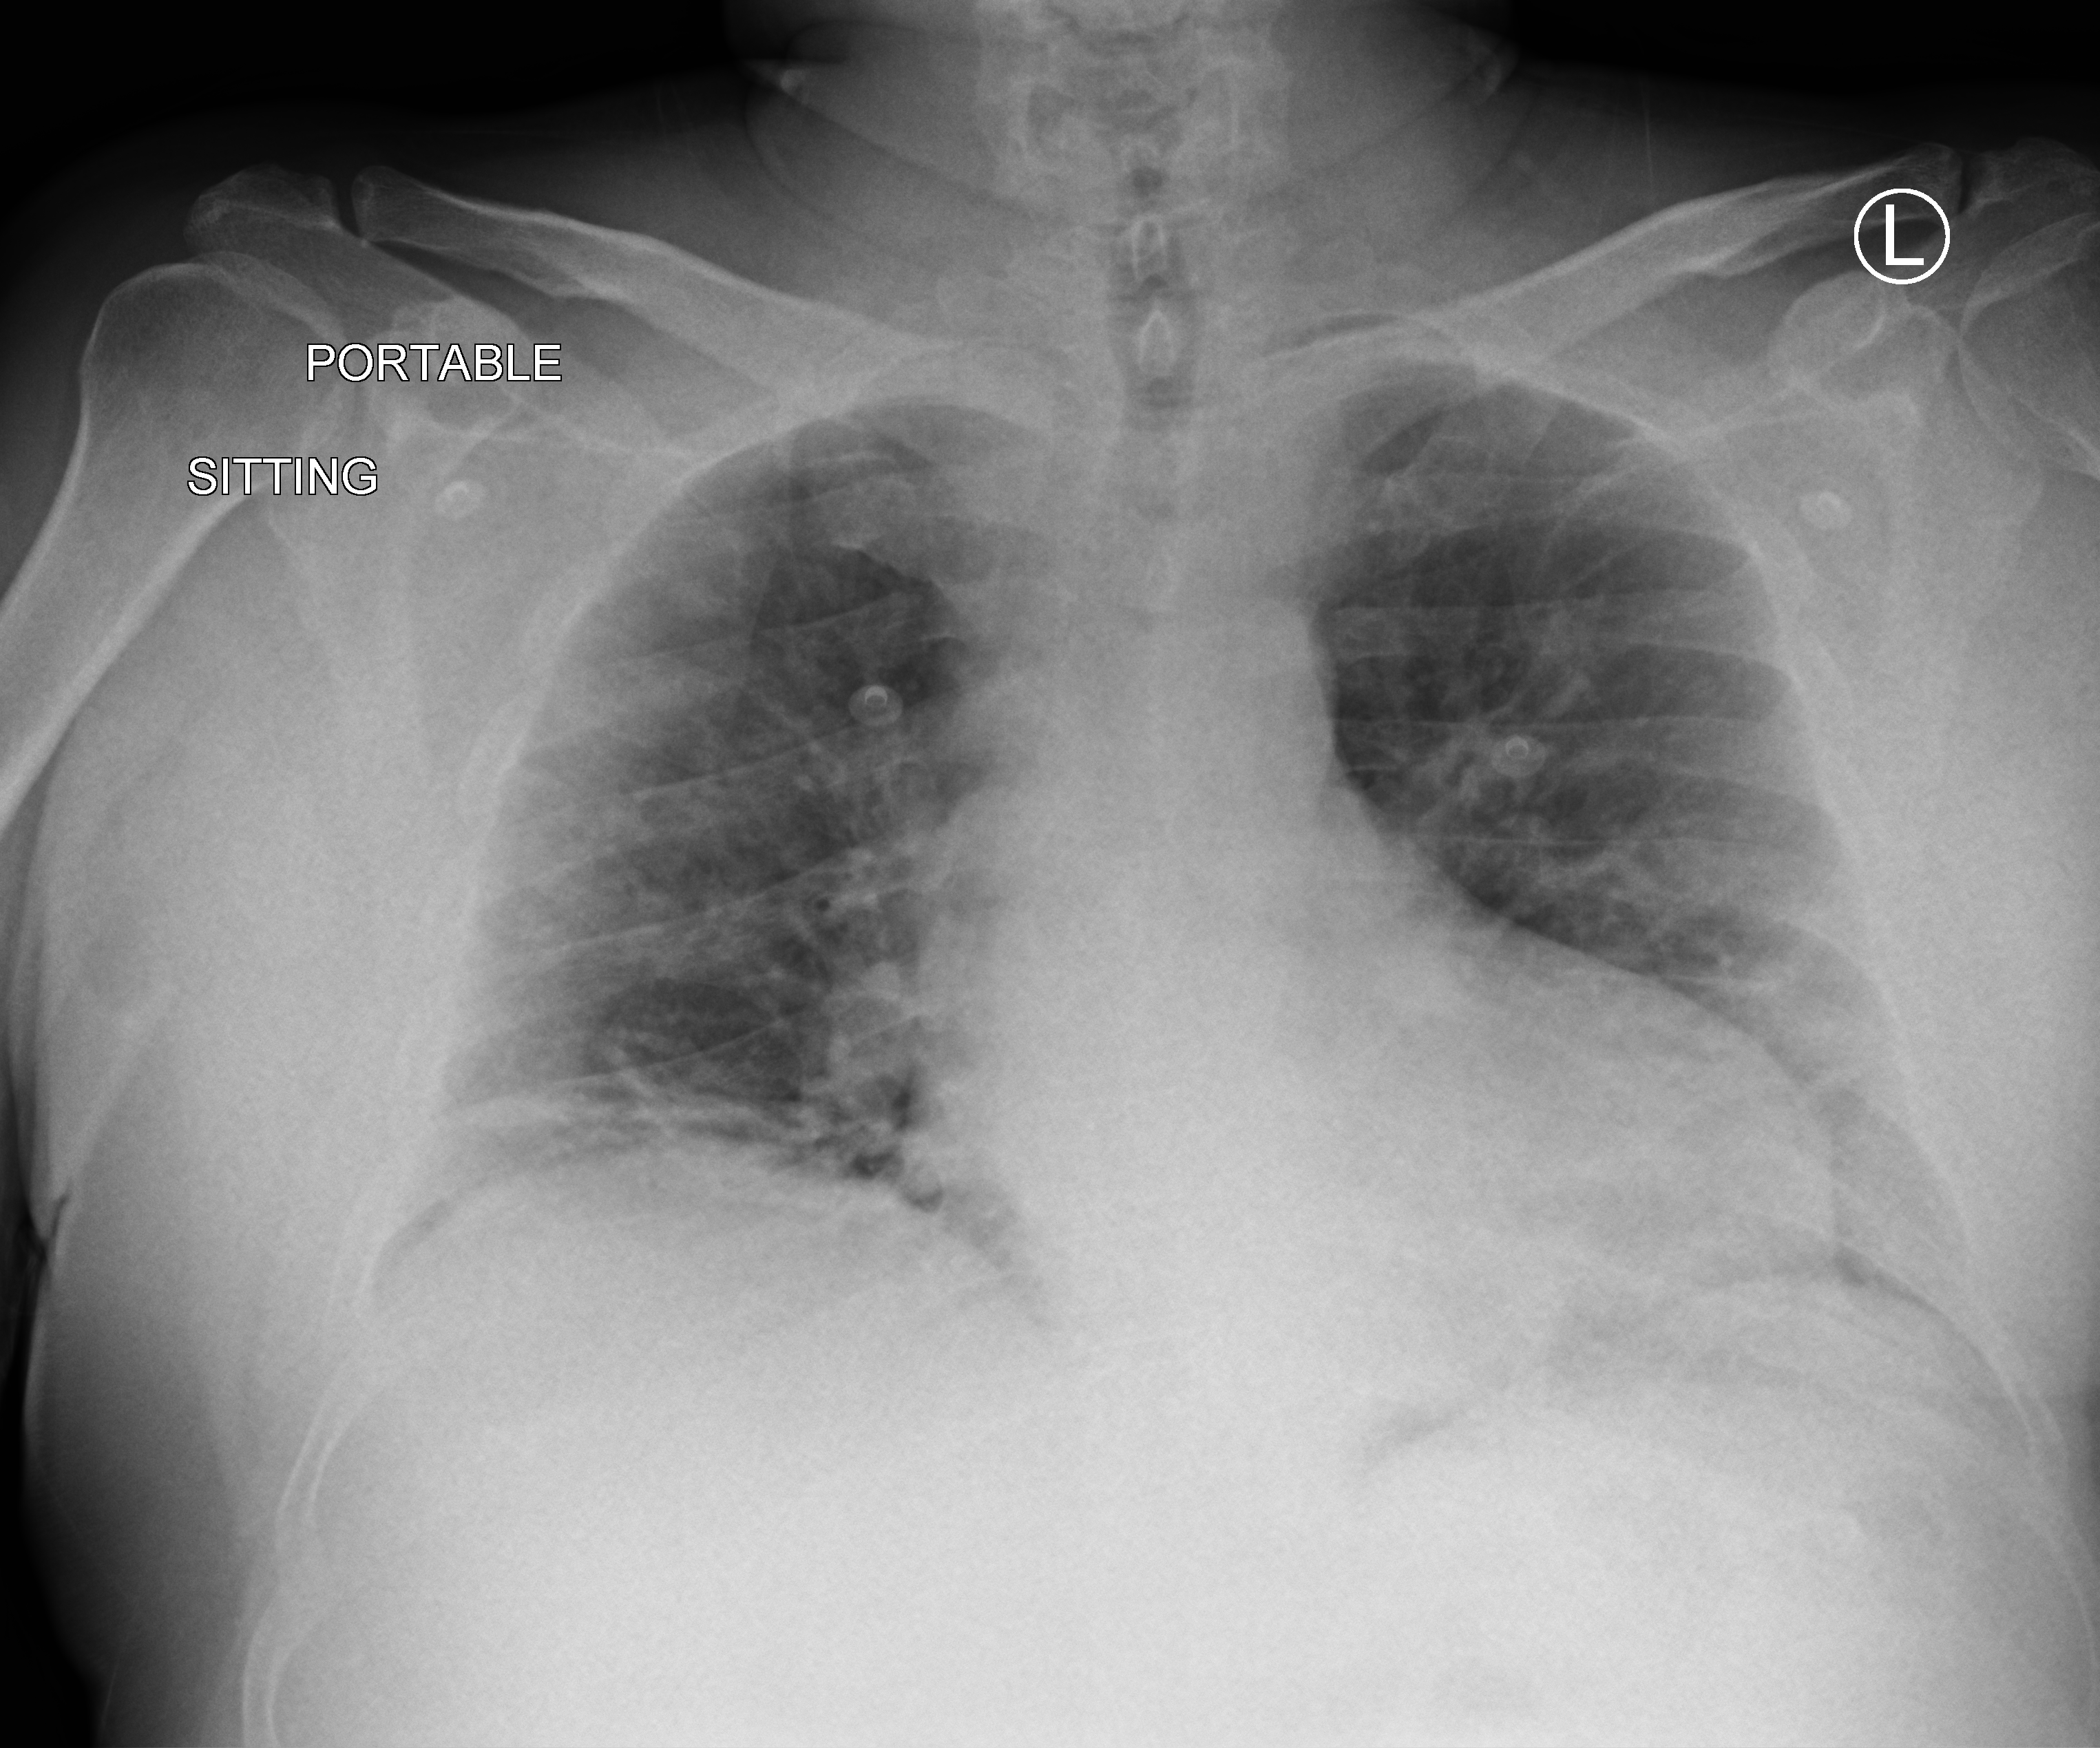
Chest X-ray (portable), anteroposterior (AP) projection. Male patient hospitalised with COVID-19, age 18–59 years.
Hospital-stay facts (about this admission, not read from this image; timing relative to this image not recorded): length of hospital stay: 17 days; chronic kidney disease (admission record): no; admitted to intensive care during this hospital stay: yes.